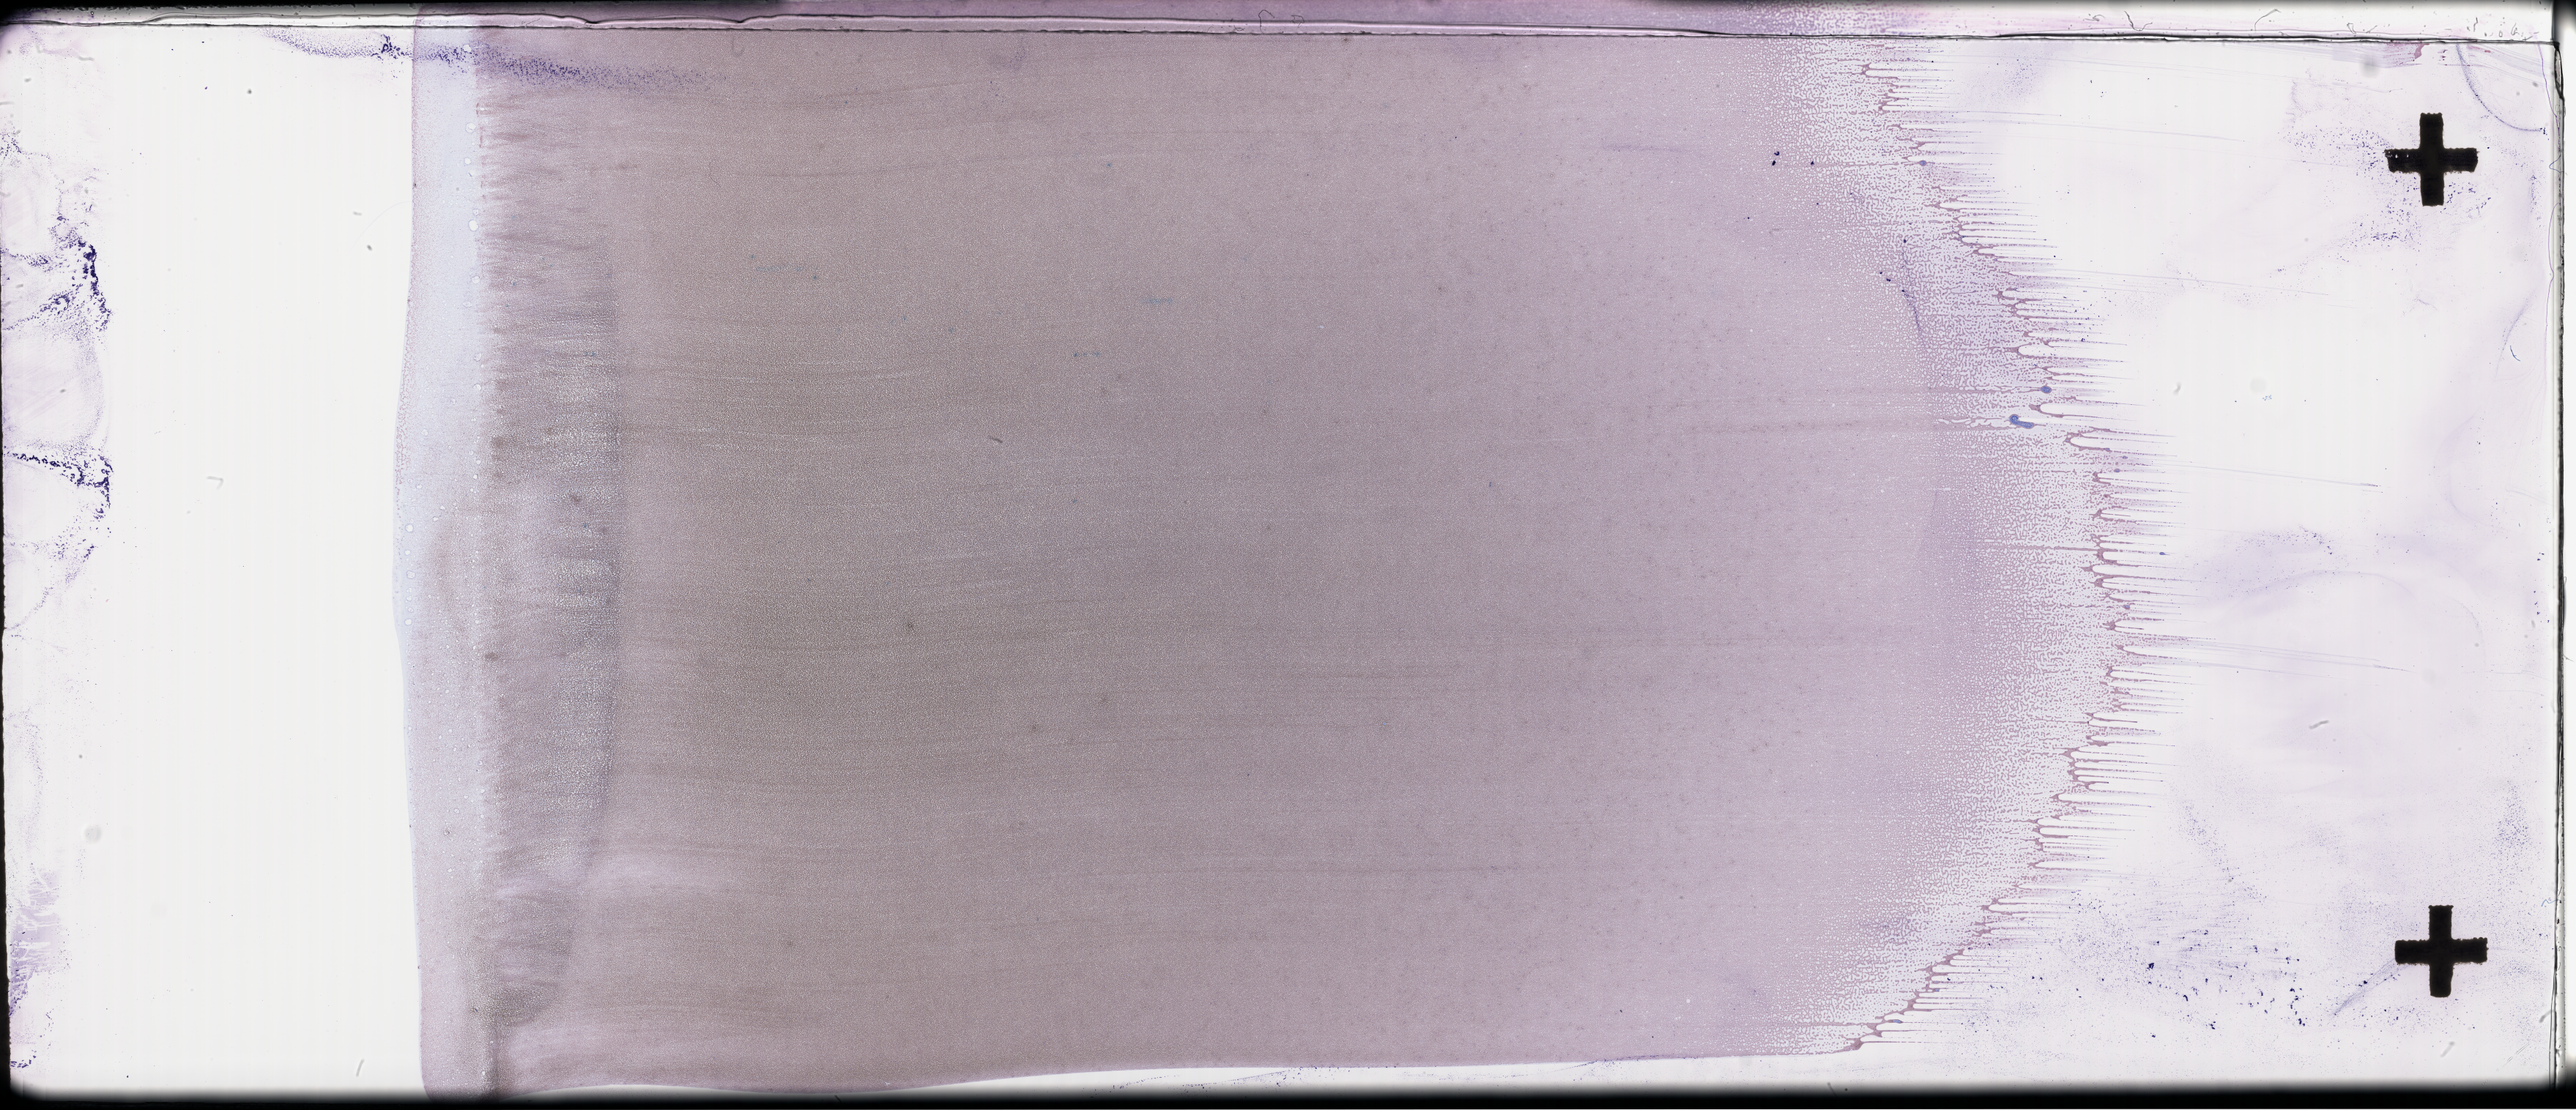
Wright-Giemsa-stained whole blood smear, whole-slide image, a low-resolution overview of the entire scanned area, about 56.8 x 24.5 mm, smear from an EDTA sample, specimen time point: collected on treatment. Male patient.
From a patient with: Plasma Cell Myeloma.